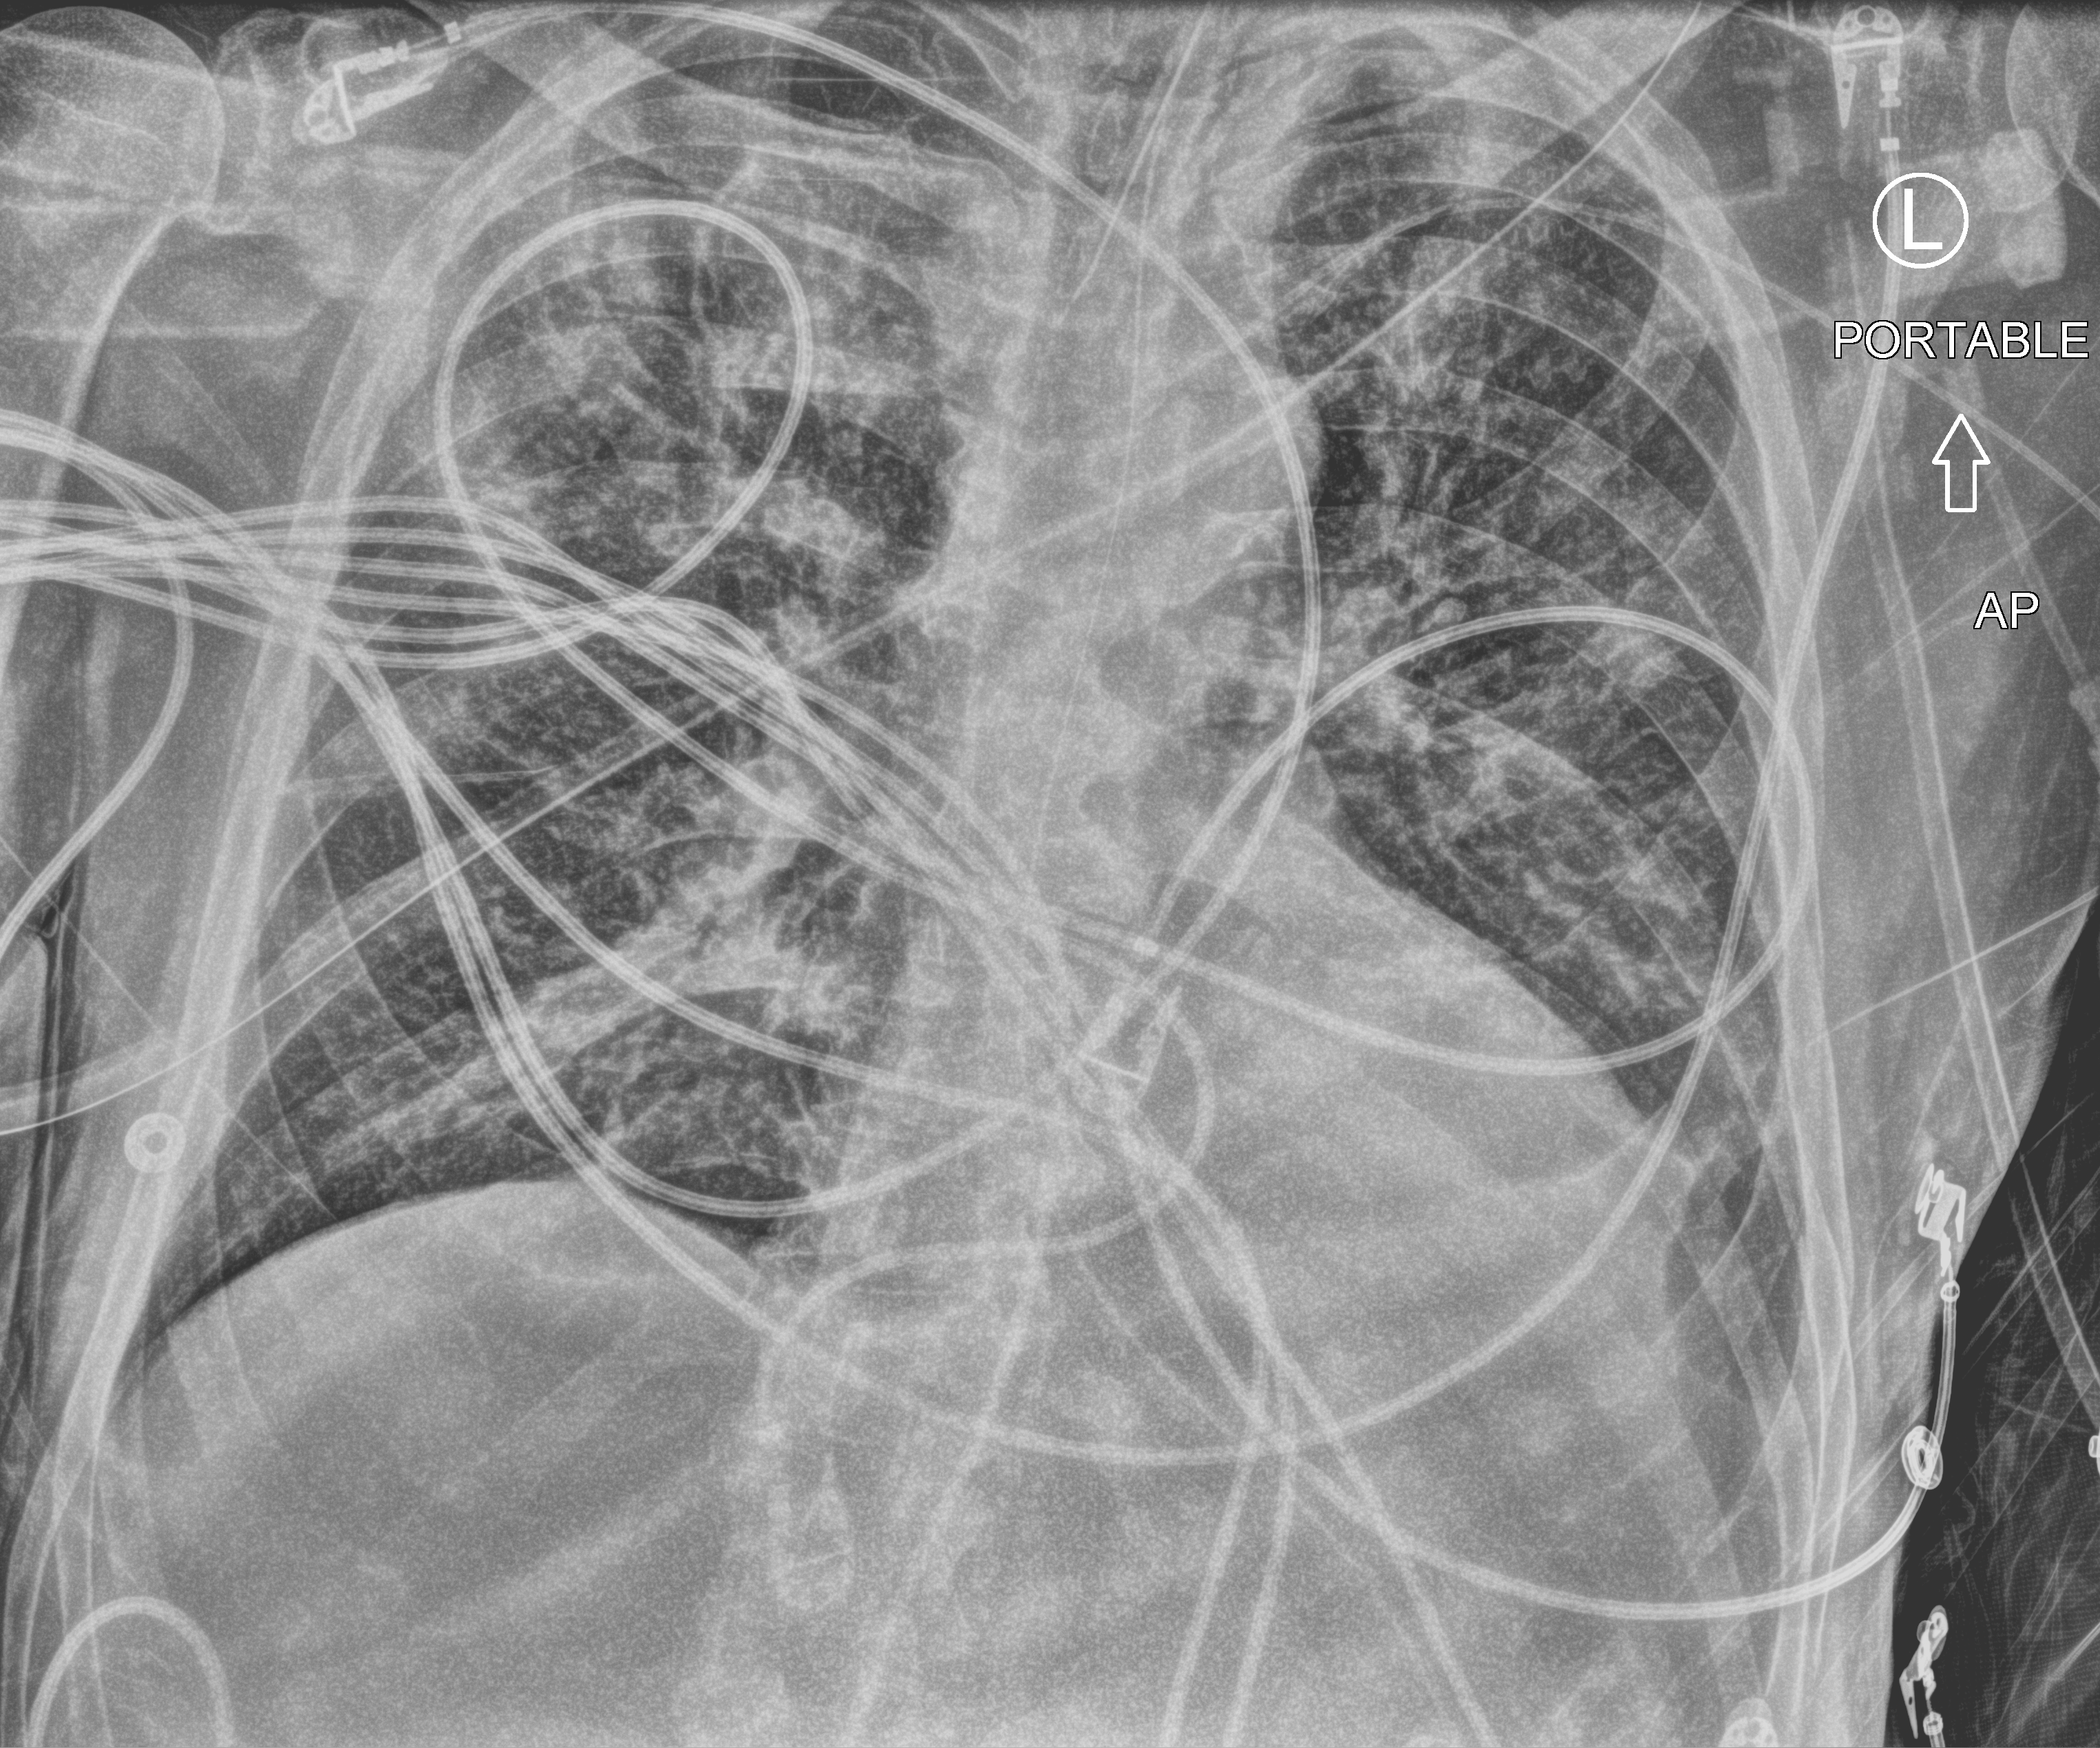
Portable chest radiograph. Male patient hospitalised with COVID-19, age 60–74 years.
Admission-level facts for this patient (not findings on this image; timing relative to this image not recorded):
- mechanically ventilated during this hospital stay: yes
- COPD (admission record): no